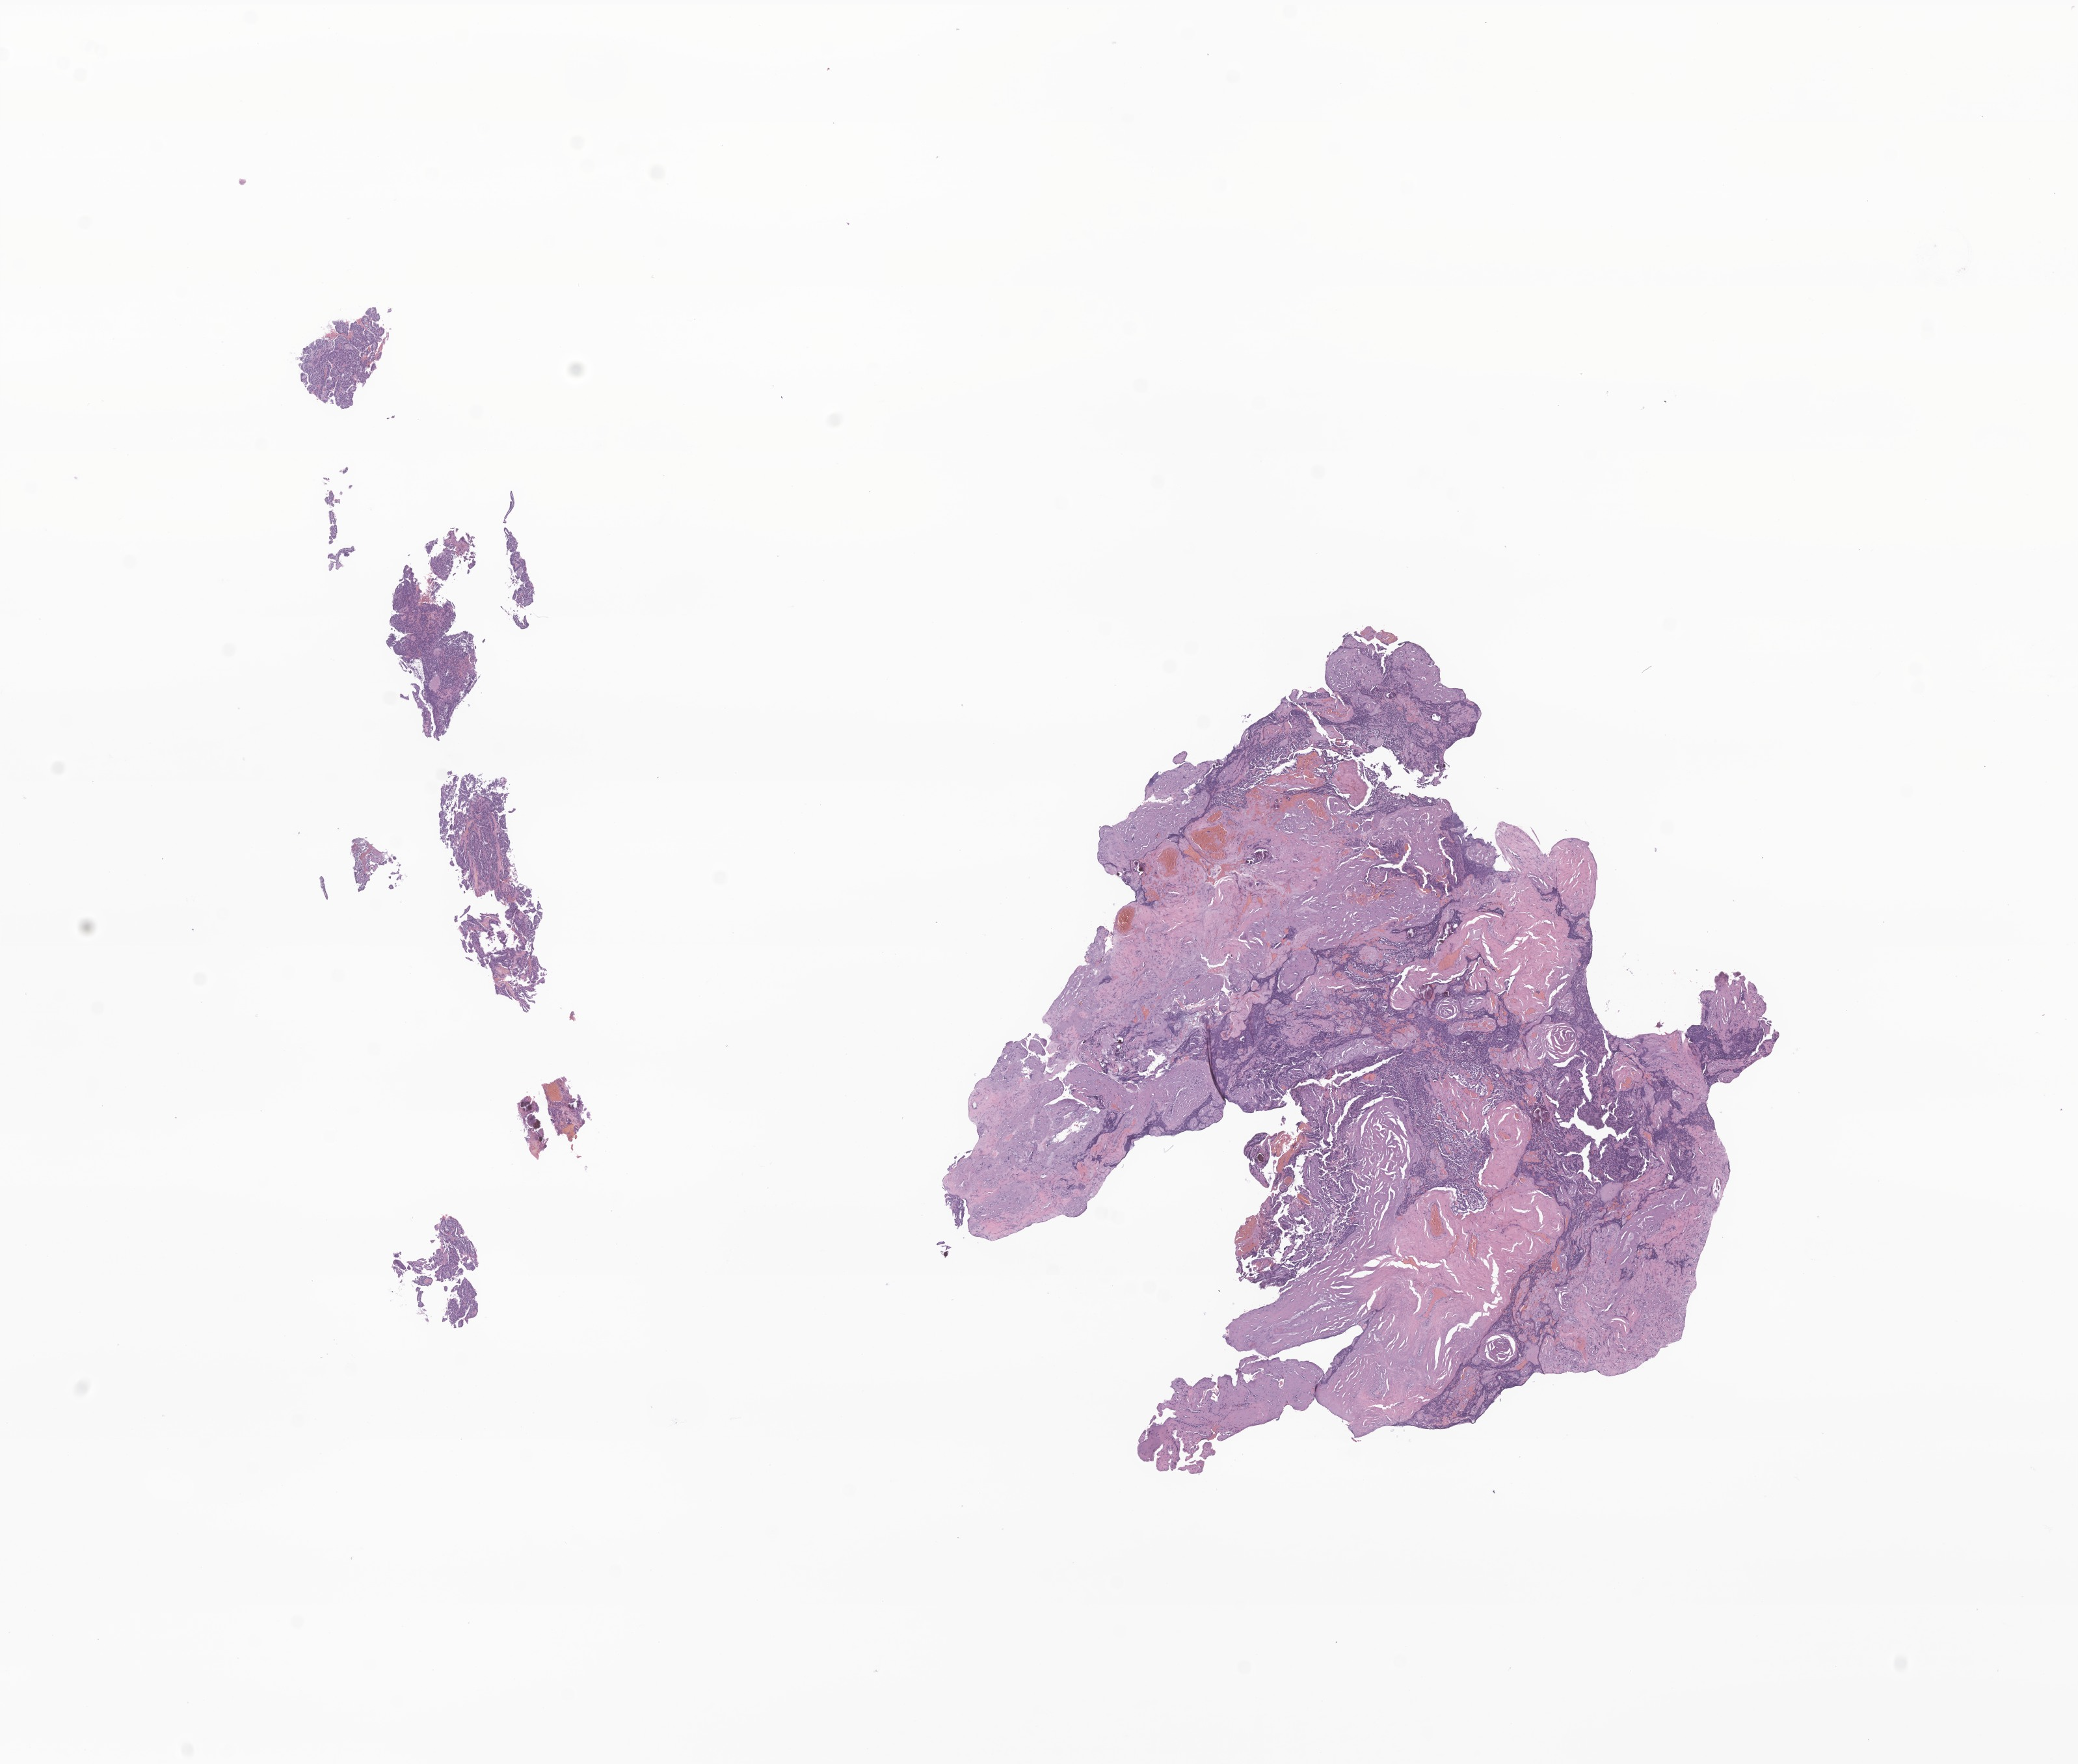
Haematoxylin and eosin whole-slide image of tumor tissue from the brain — a low-resolution overview of the entire scanned area, about 13.5 x 11.4 mm, FFPE section. Patient: female, age 208 months (17 years 4 months).
Diagnosis (ICD-O-3 morphology term): Ependymoma, NOS.